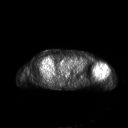
FDG PET of an extremity soft-tissue mass (from a PET/CT study), one axial slice. Position 149 of 267 along the scan axis. 3.27 mm slice thickness. 128 × 128 image matrix, field of view 700 × 700 mm. Patient: female, 83 years. Case-level facts recorded for this patient, not image findings: histological type: pleiomorphic leiomyosarcoma; grade: high; site of the primary tumour: left biceps.
Structures marked on this image (expert contour drawn on MRI and transferred to this co-registered scan by the dataset authors):
- gross tumour volume including surrounding oedema: box from (x=92, y=62) to (x=107, y=77) px
- gross tumour volume (mass): (x=92, y=62)–(x=107, y=77)